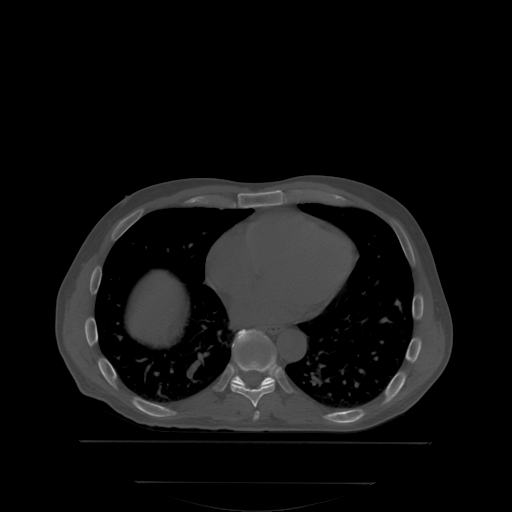
CT including the spine, one axial slice. Slice 212 of 350 in the series (ordered by position). Bone window (W 1800 / L 400 HU). 512 × 512 image matrix, field of view 500 × 500 mm. Patient: male, 58 years. Case-level facts recorded for this patient, not image findings: primary cancer: prostate; vertebrae with lytic lesions (as recorded): L1.
Annotated regions visible in this slice (semi-automatic segmentation, software-assisted and operator-edited):
- T7 vertebra: bounding box [x1, y1, x2, y2] px = [255, 412, 259, 417]
- T8 vertebra: [231, 357, 277, 407]
- T9 vertebra: [232, 331, 275, 387]